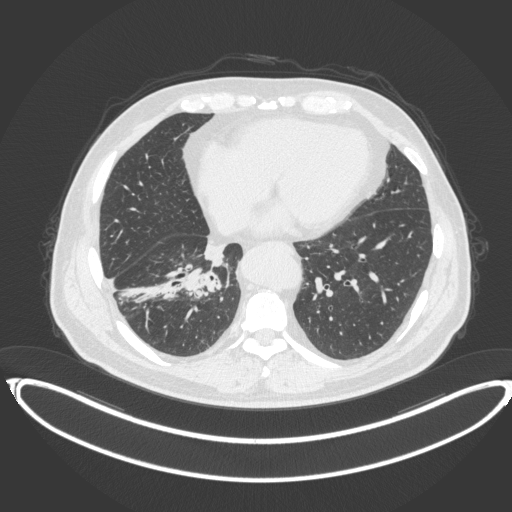
Chest CT, one axial slice; slice 145 of 383 in the series (ordered by position); reconstruction kernel B31f; 120 kVp; lung window (W 1500 / L -600 HU); 1 mm slice thickness; 512 × 512 image matrix, field of view 448 × 448 mm. Patient: male, 61 years. Case-level facts recorded for this patient, not image findings: clinical TNM (as recorded): T1b N1 M0.
Structures marked on this image (rectangle marked by the reading radiologist):
- lung tumour (recorded histology: squamous cell carcinoma): bounding box [x1, y1, x2, y2] px = [178, 262, 225, 301]